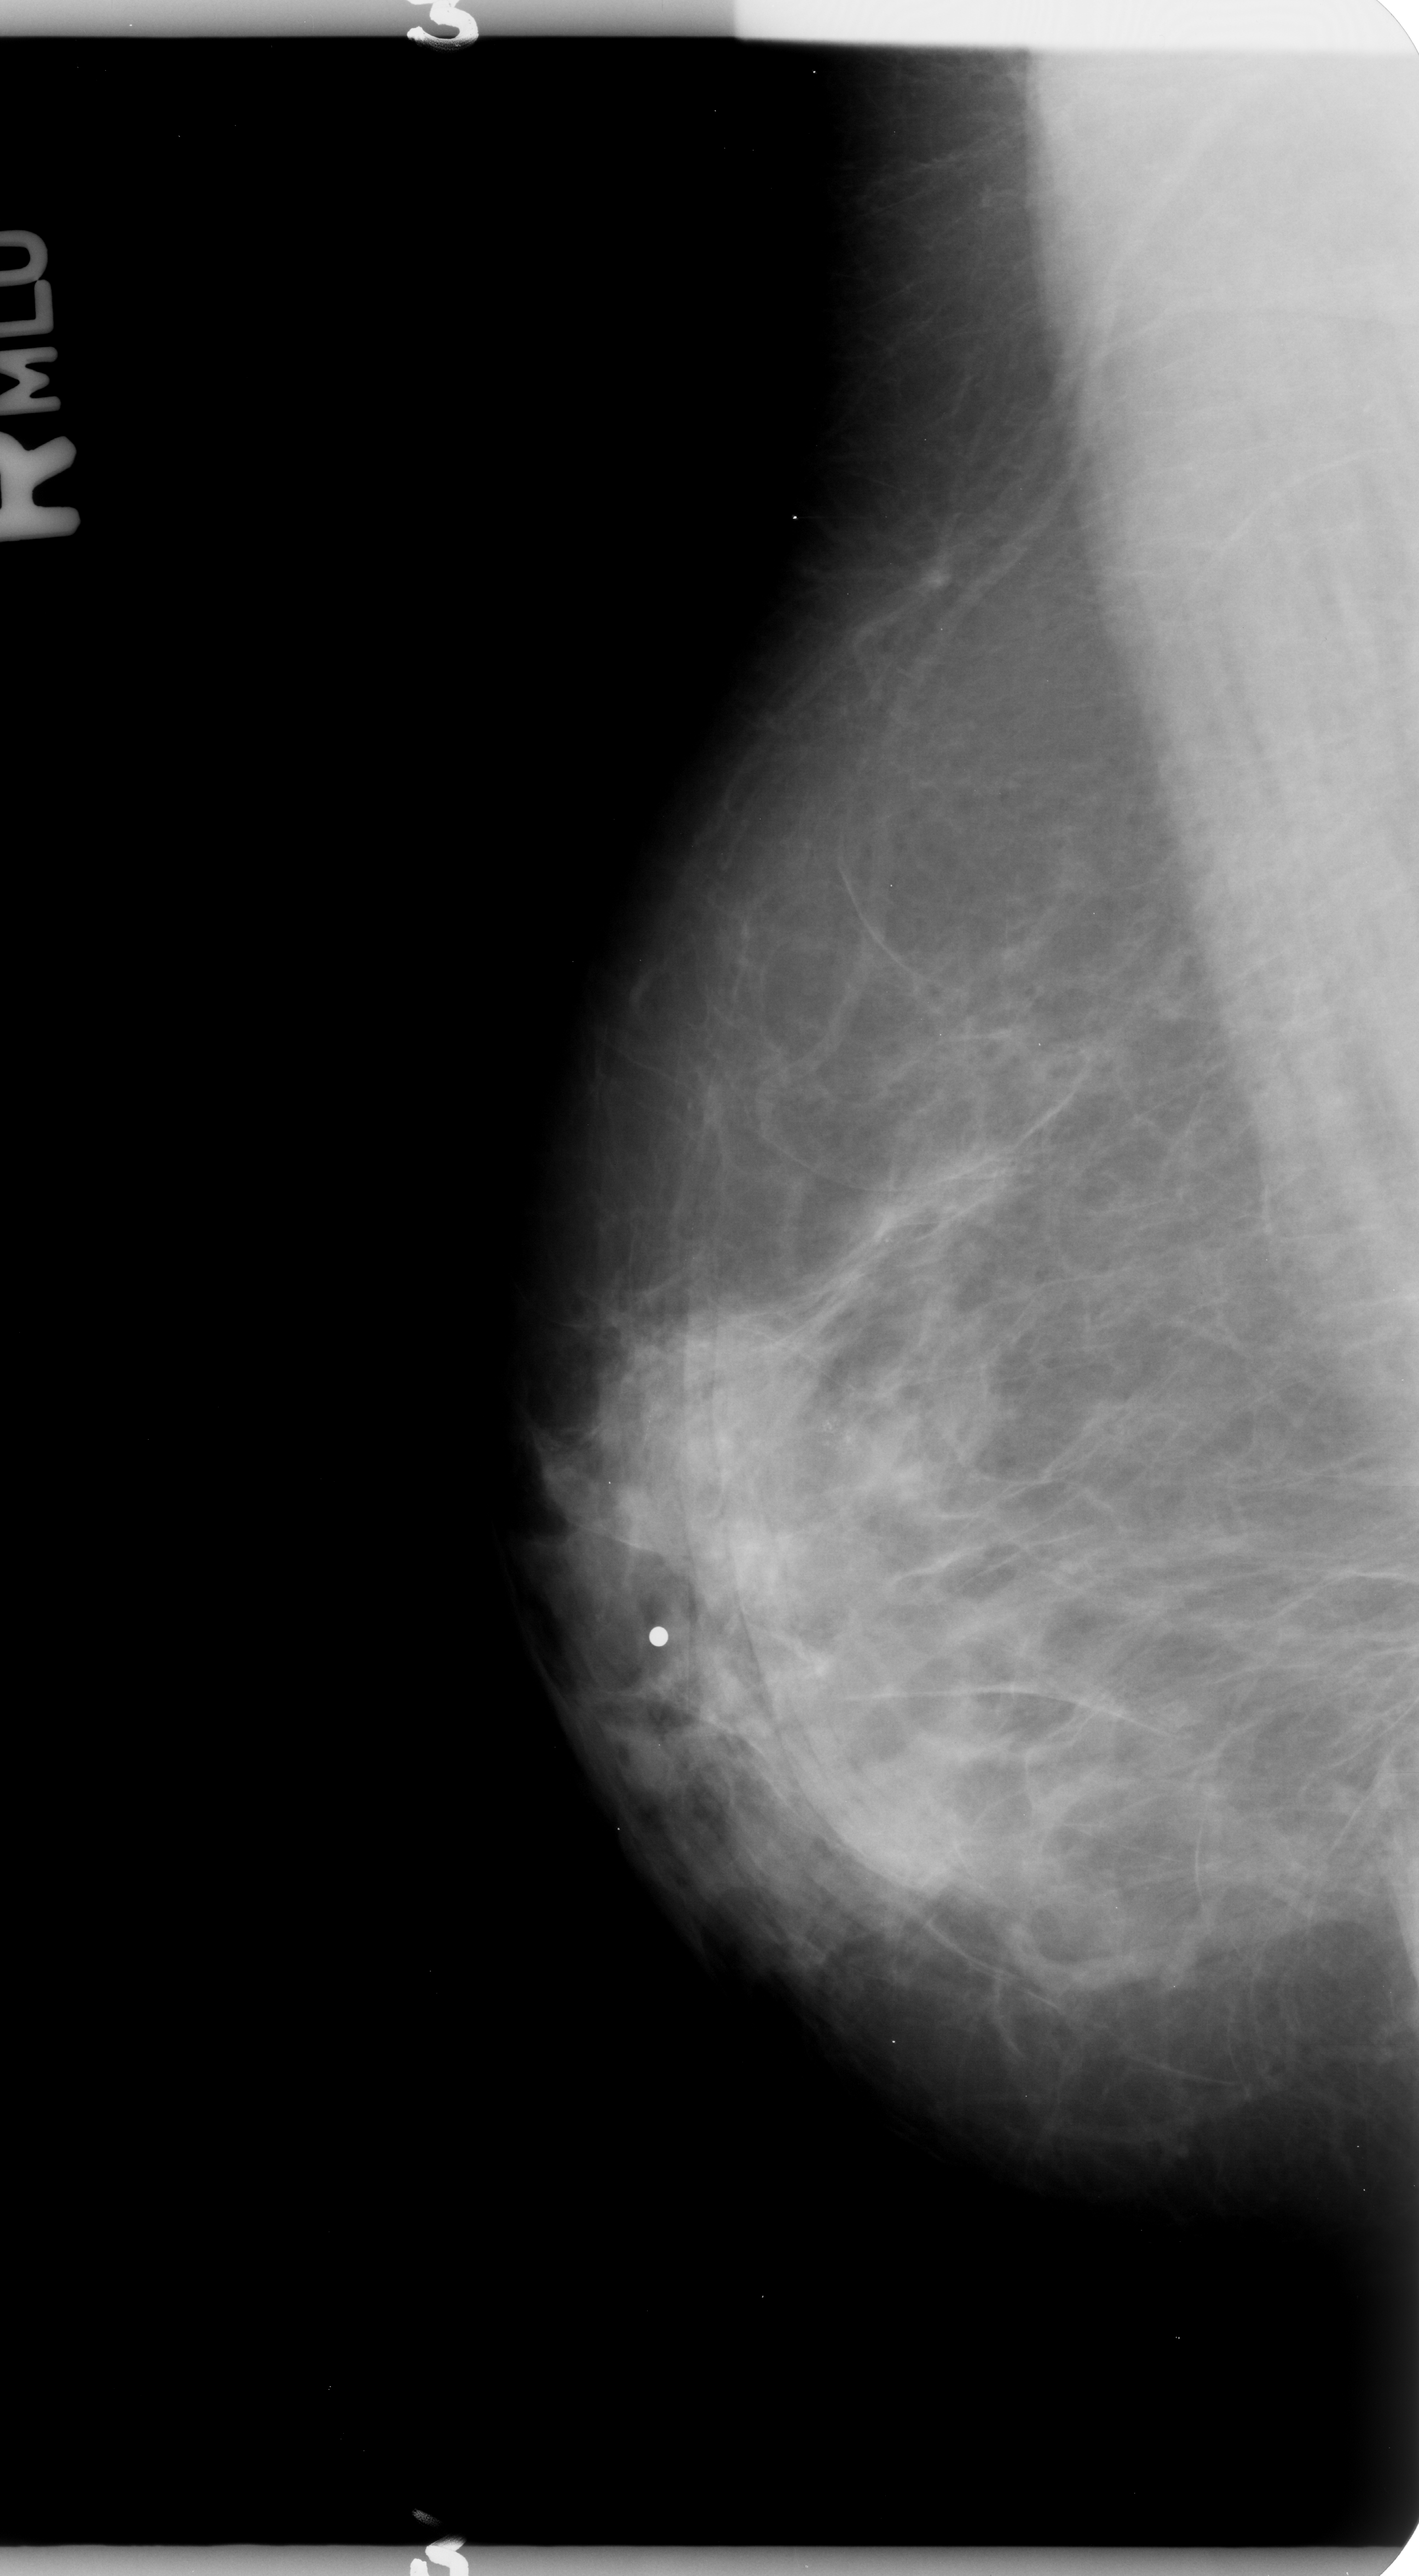
Scanned film-screen mammogram; right breast; mediolateral oblique (MLO) view; breast composition: heterogeneously dense (BI-RADS density category 3 of 4); 1419 × 2576 image matrix.
Expert-marked regions of interest on this image (one box per marked abnormality):
- calcifications, morphology pleomorphic, distribution clustered; BI-RADS assessment category 4; subtlety rating 3 on a 1 (subtle) to 5 (obvious) scale; pathology result (as recorded, not read from the image): benign: bounding box [x1, y1, x2, y2] px = [783, 1375, 899, 1495]